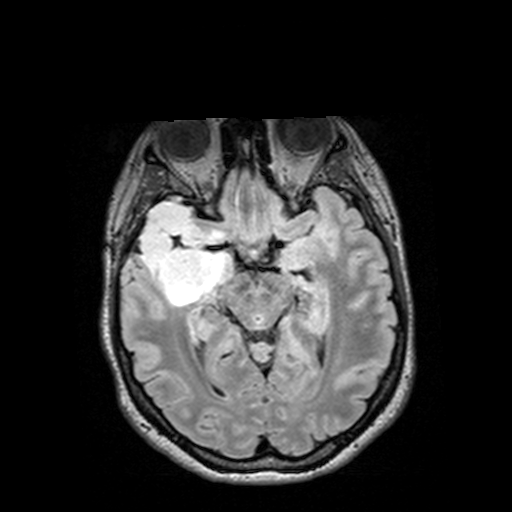
Brain MRI from a brain-tumour surgery series, one axial slice; position 84 of 144 along the scan axis; T2 FLAIR; 1 mm slice thickness; 512 × 512 image matrix, field of view 250 × 250 mm. From the clinical record (not read from this slice): histopathology: Astrocytoma; WHO grade: 3; IDH mutation: yes; tumour location: Right Insular Temporal.
Annotated regions visible in this slice (expert manual segmentation):
- tumour: bounding box <126,200,232,305> (left, top, right, bottom; pixels)